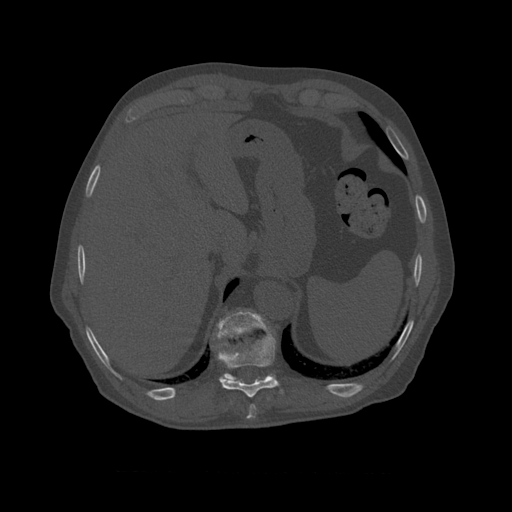
CT including the spine, one axial slice; 120 kVp; bone window (W 1800 / L 400 HU); 1.25 mm slice thickness; 512 × 512 image matrix, field of view 405 × 405 mm. Patient age 75 years. From the clinical record (not read from this slice): primary cancer: prostate.
Outlined on this slice (semi-automatically segmented with operator editing):
- T10 vertebra: box from (x=214, y=310) to (x=275, y=380) px
- T8 vertebra: (x=249, y=404)–(x=257, y=411)
- T9 vertebra: (x=216, y=326)–(x=284, y=398)